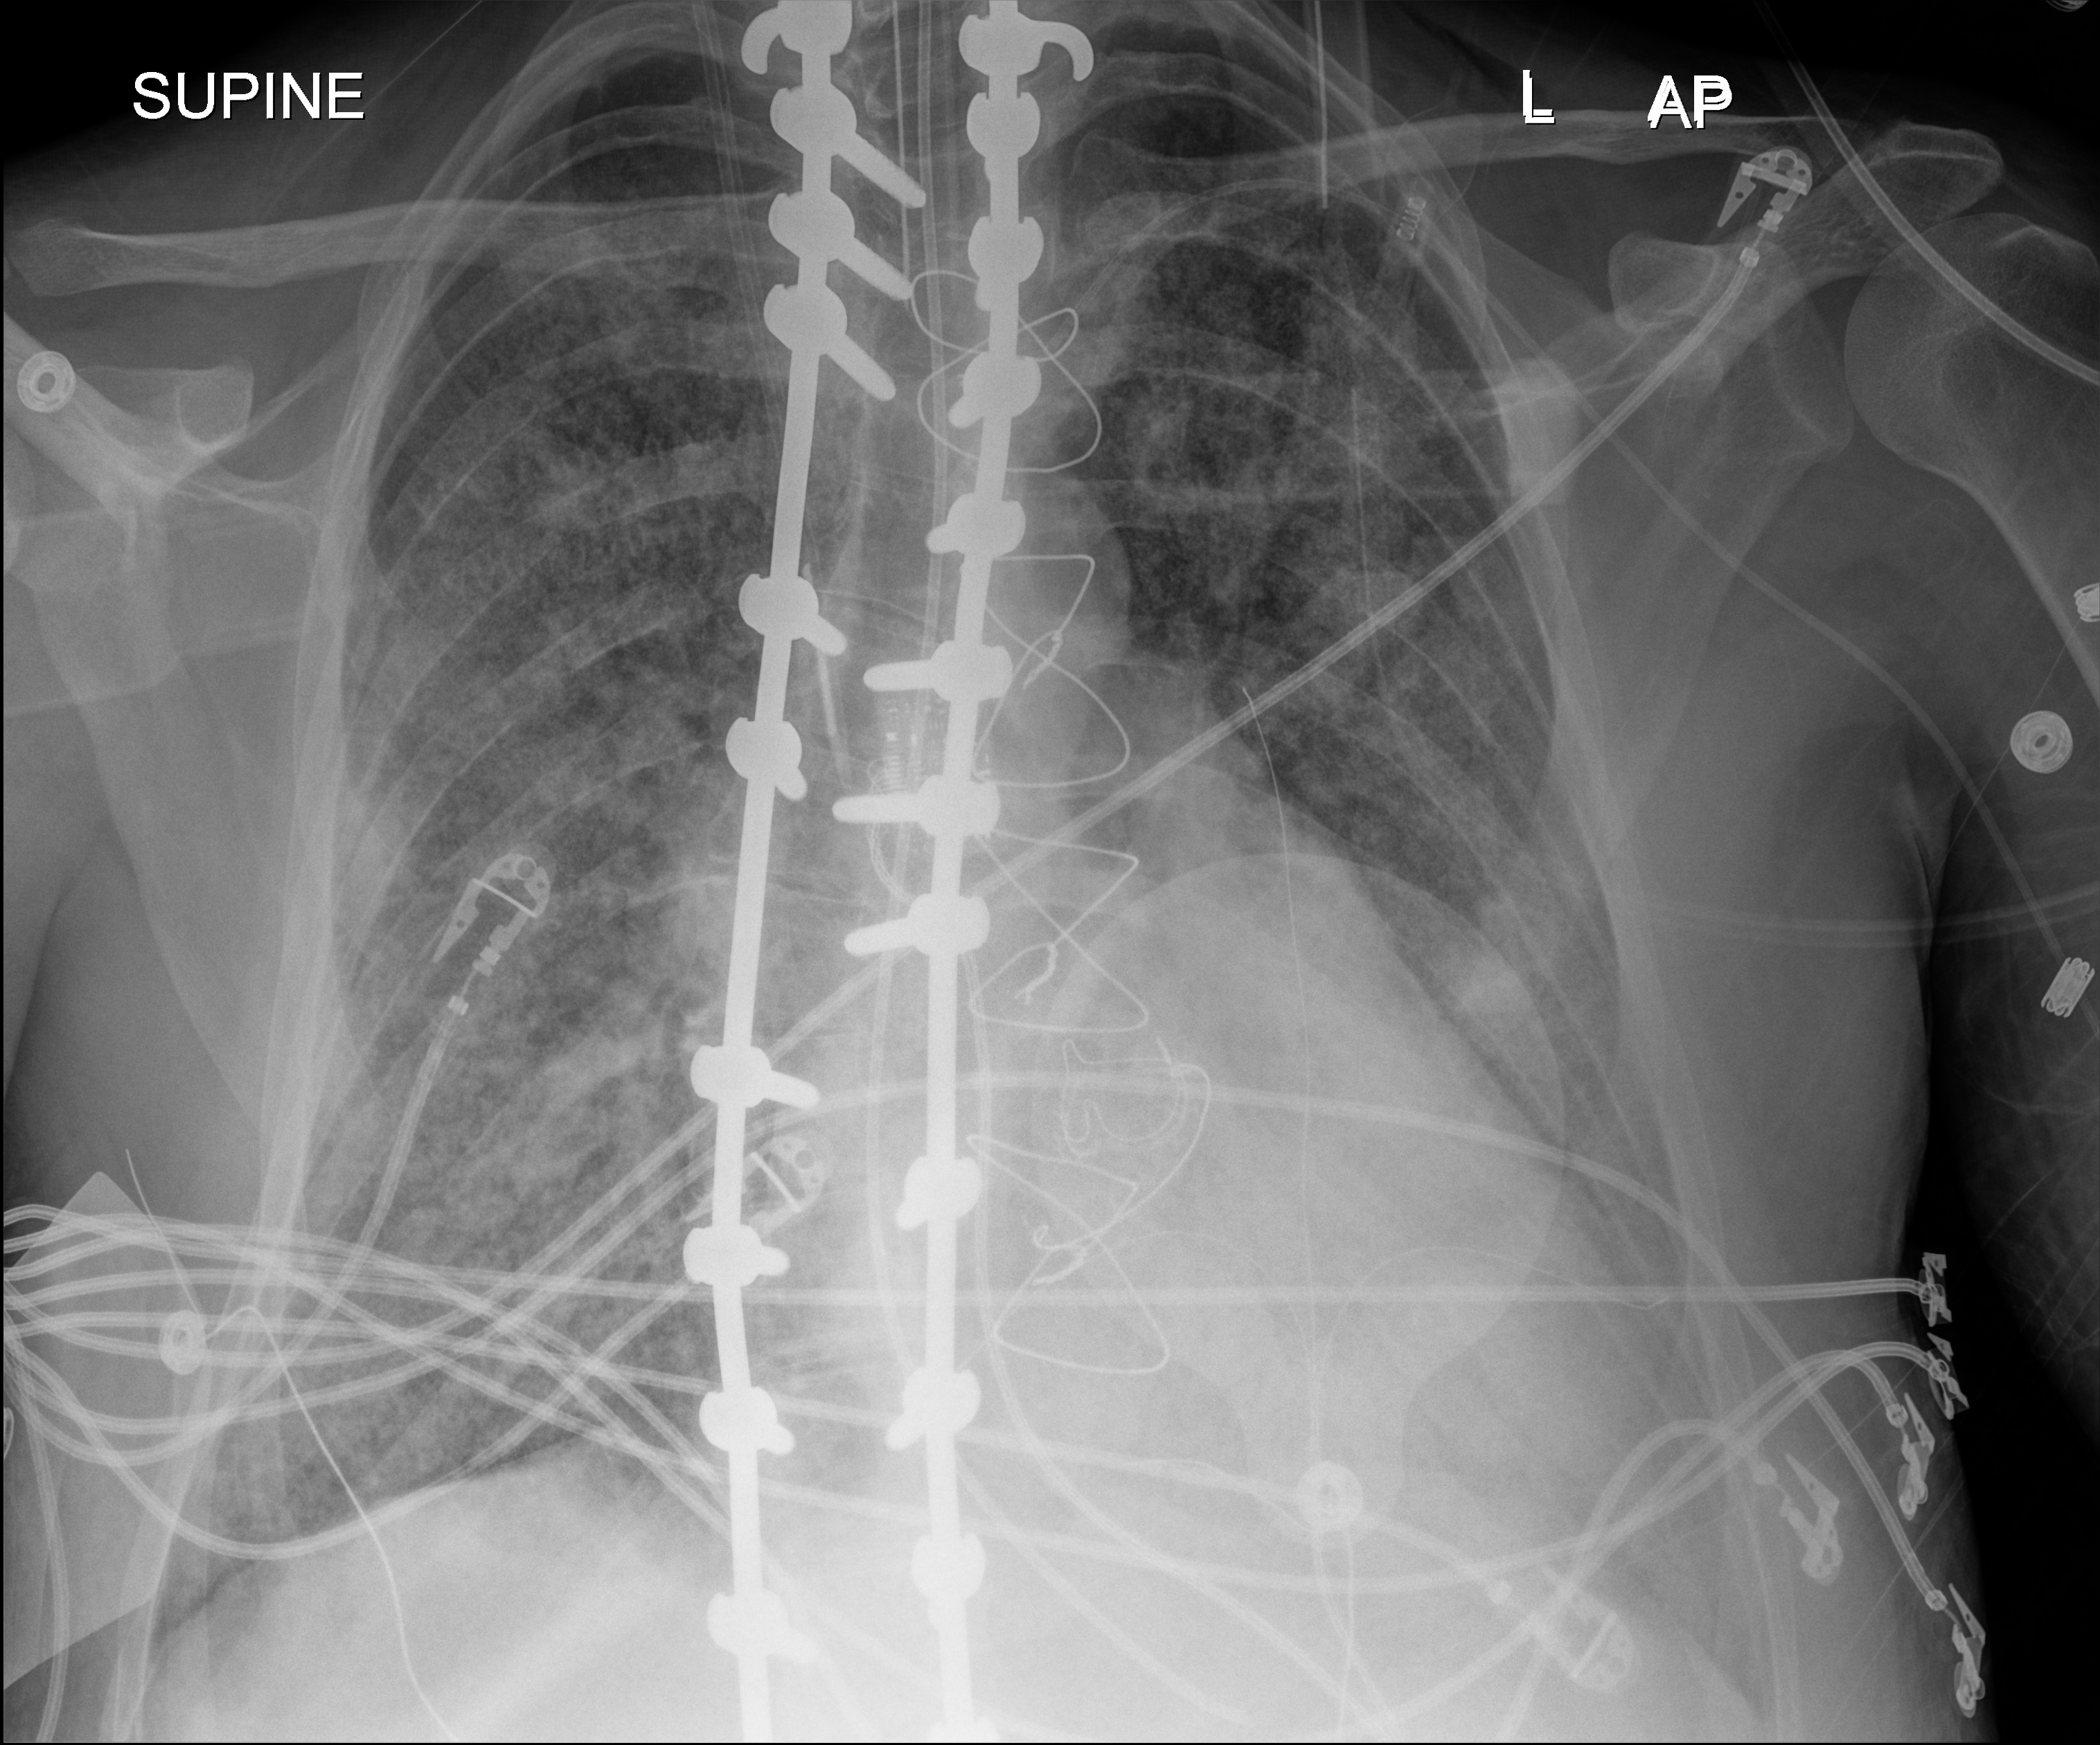
Chest X-ray (portable). Patient hospitalised with COVID-19, aged 18–59 years.
From the hospital-stay record, not from the radiograph (when in the stay this image was taken is not recorded): diabetes (admission record): no.